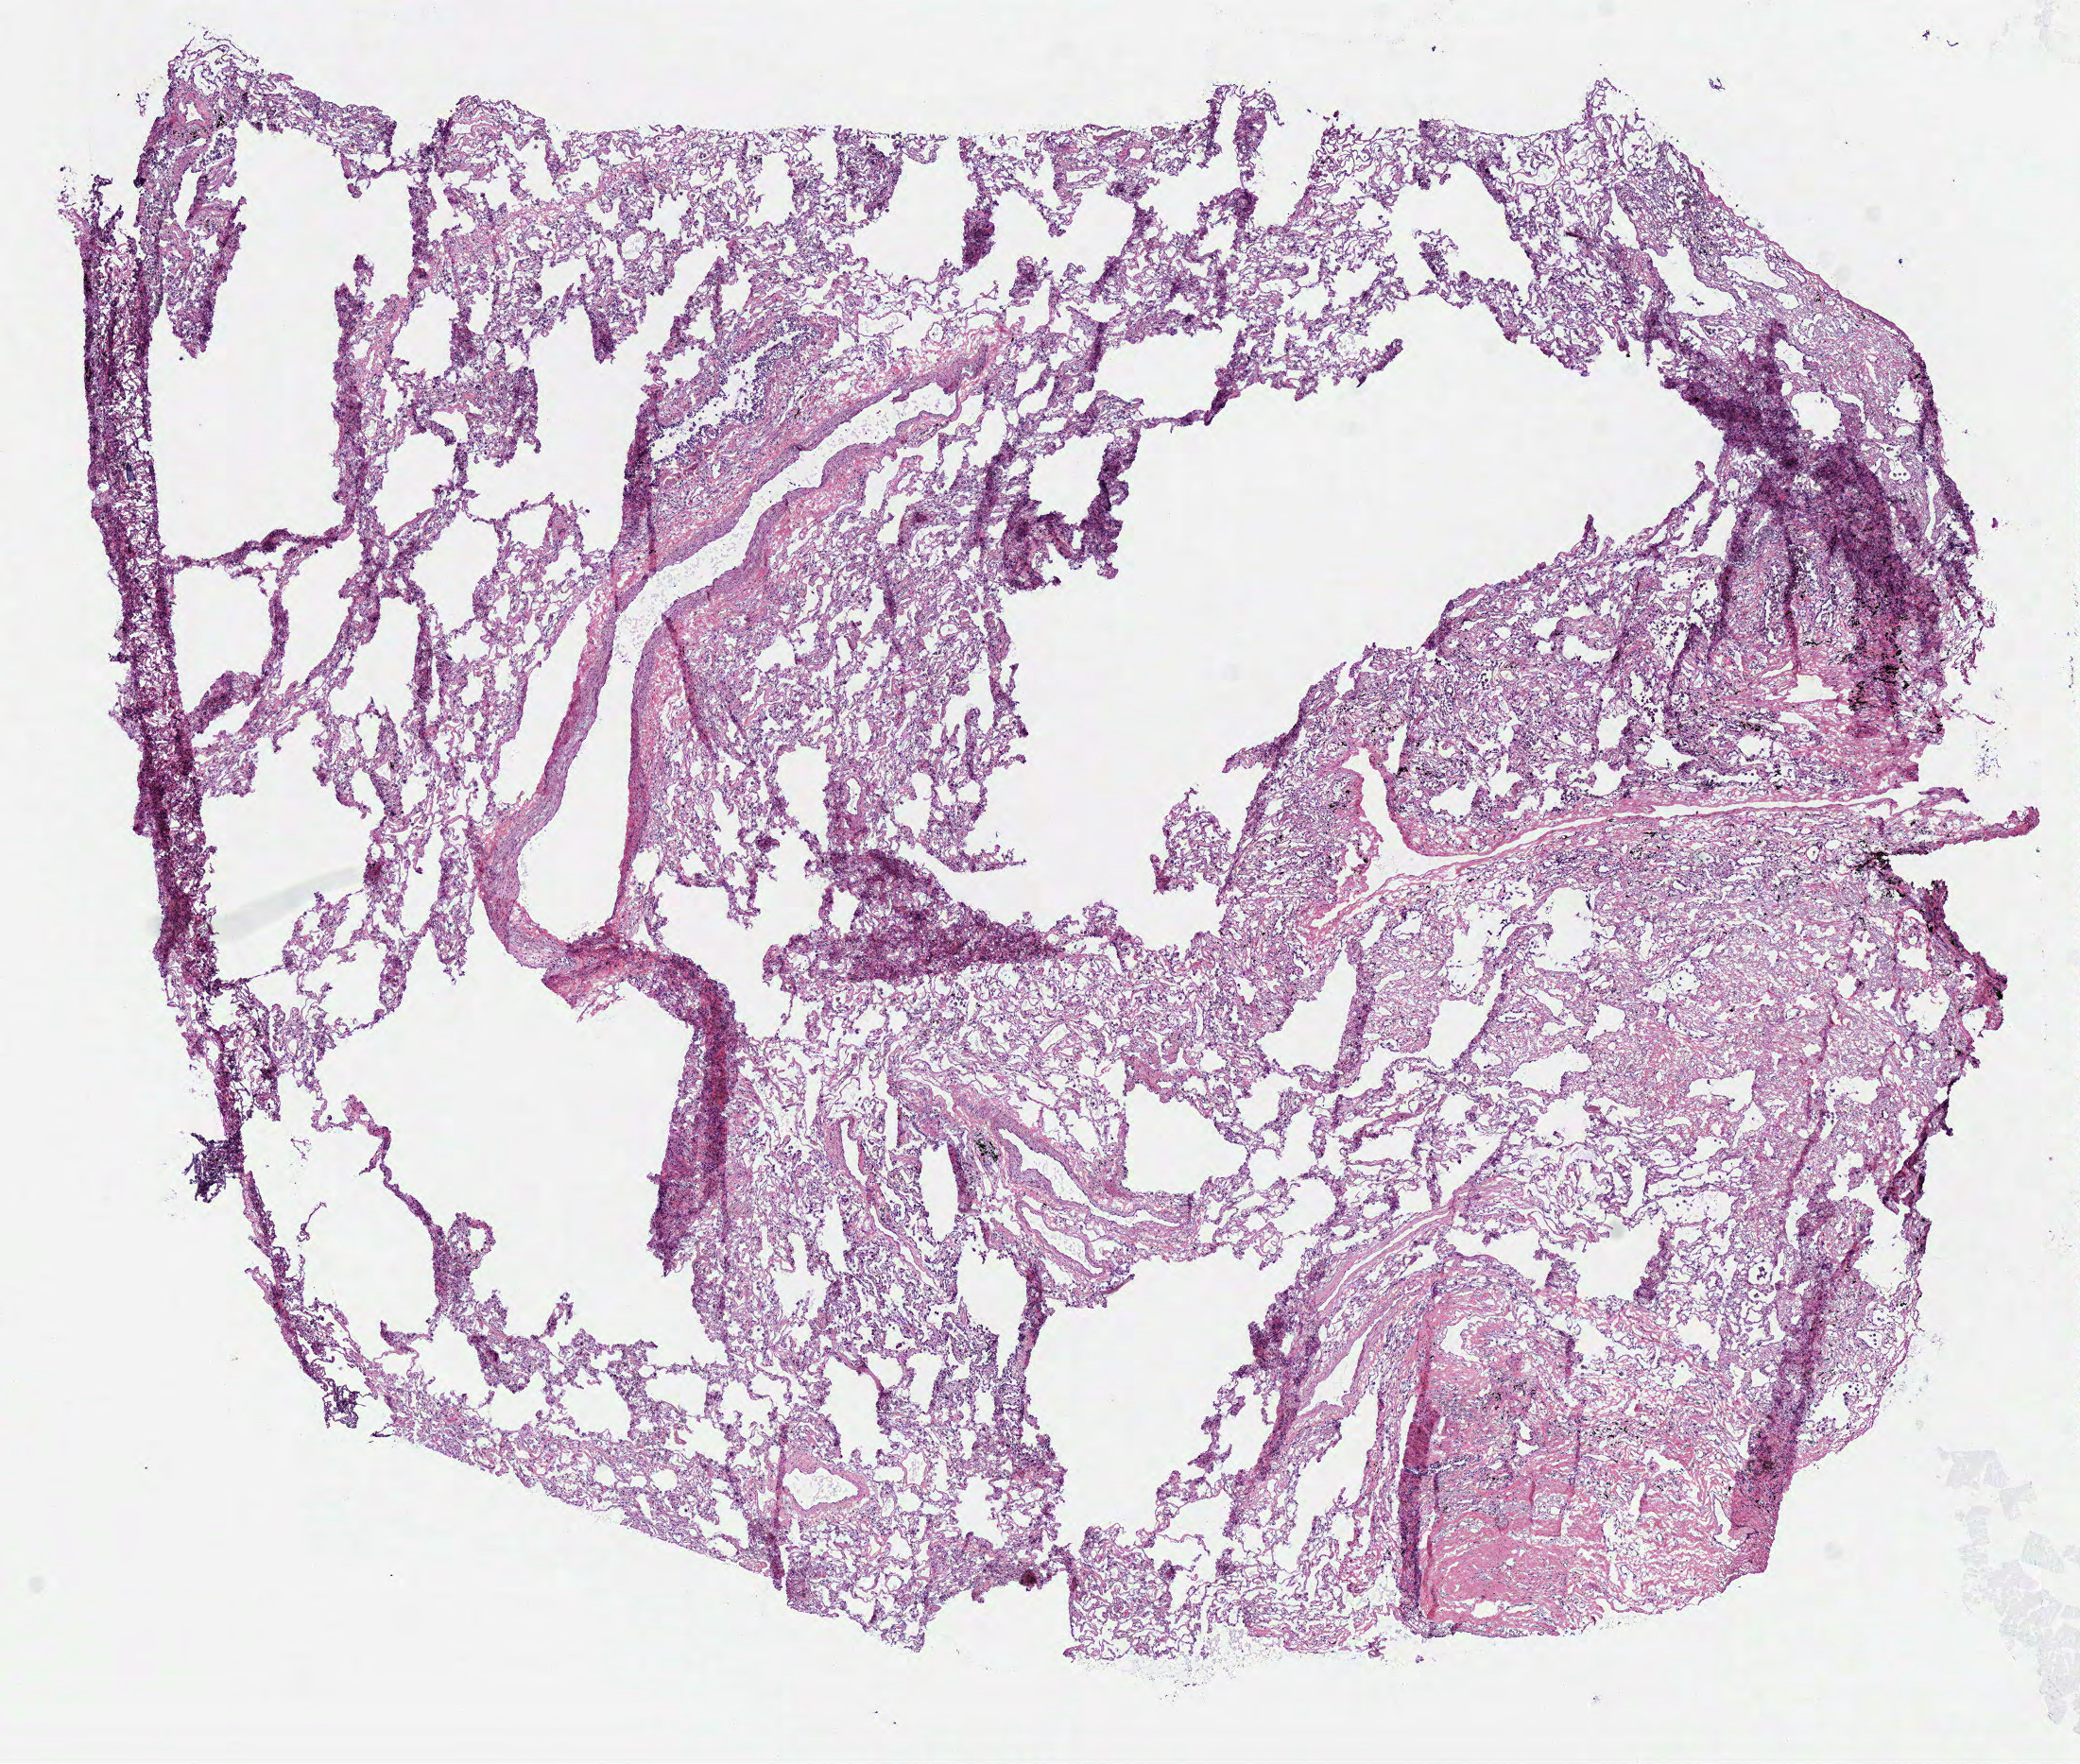
Digitized Hematoxylin and eosin (H&E) stained tissue section (whole slide) — whole scanned area (about 8.7 x 7.4 mm) shown as a low-resolution overview. Frozen section from the top of the tissue portion. Lung, solid tissue normal (non-tumour tissue) sample. Female, age 64 years at initial diagnosis.
This section: solid tissue normal sample (biorepository sample class). Patient diagnosis: Adenocarcinoma with mixed subtypes (upper lobe, lung).